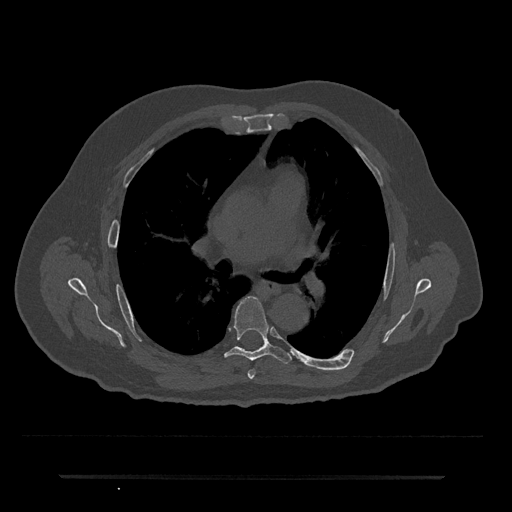
CT including the spine, one axial slice. Position 440 of 797 along the scan axis. 120 kVp. Bone window (W 1800 / L 400 HU). 512 × 512 image matrix, field of view 437 × 437 mm. Male patient, age 69 years. From the clinical record (not read from this slice): primary cancer: prostate.
Outlined on this slice (semi-automatic segmentation, software-assisted and operator-edited):
- T5 vertebra: bounding box <248,369,255,379> (left, top, right, bottom; pixels)
- T6 vertebra: <225,297,292,364>